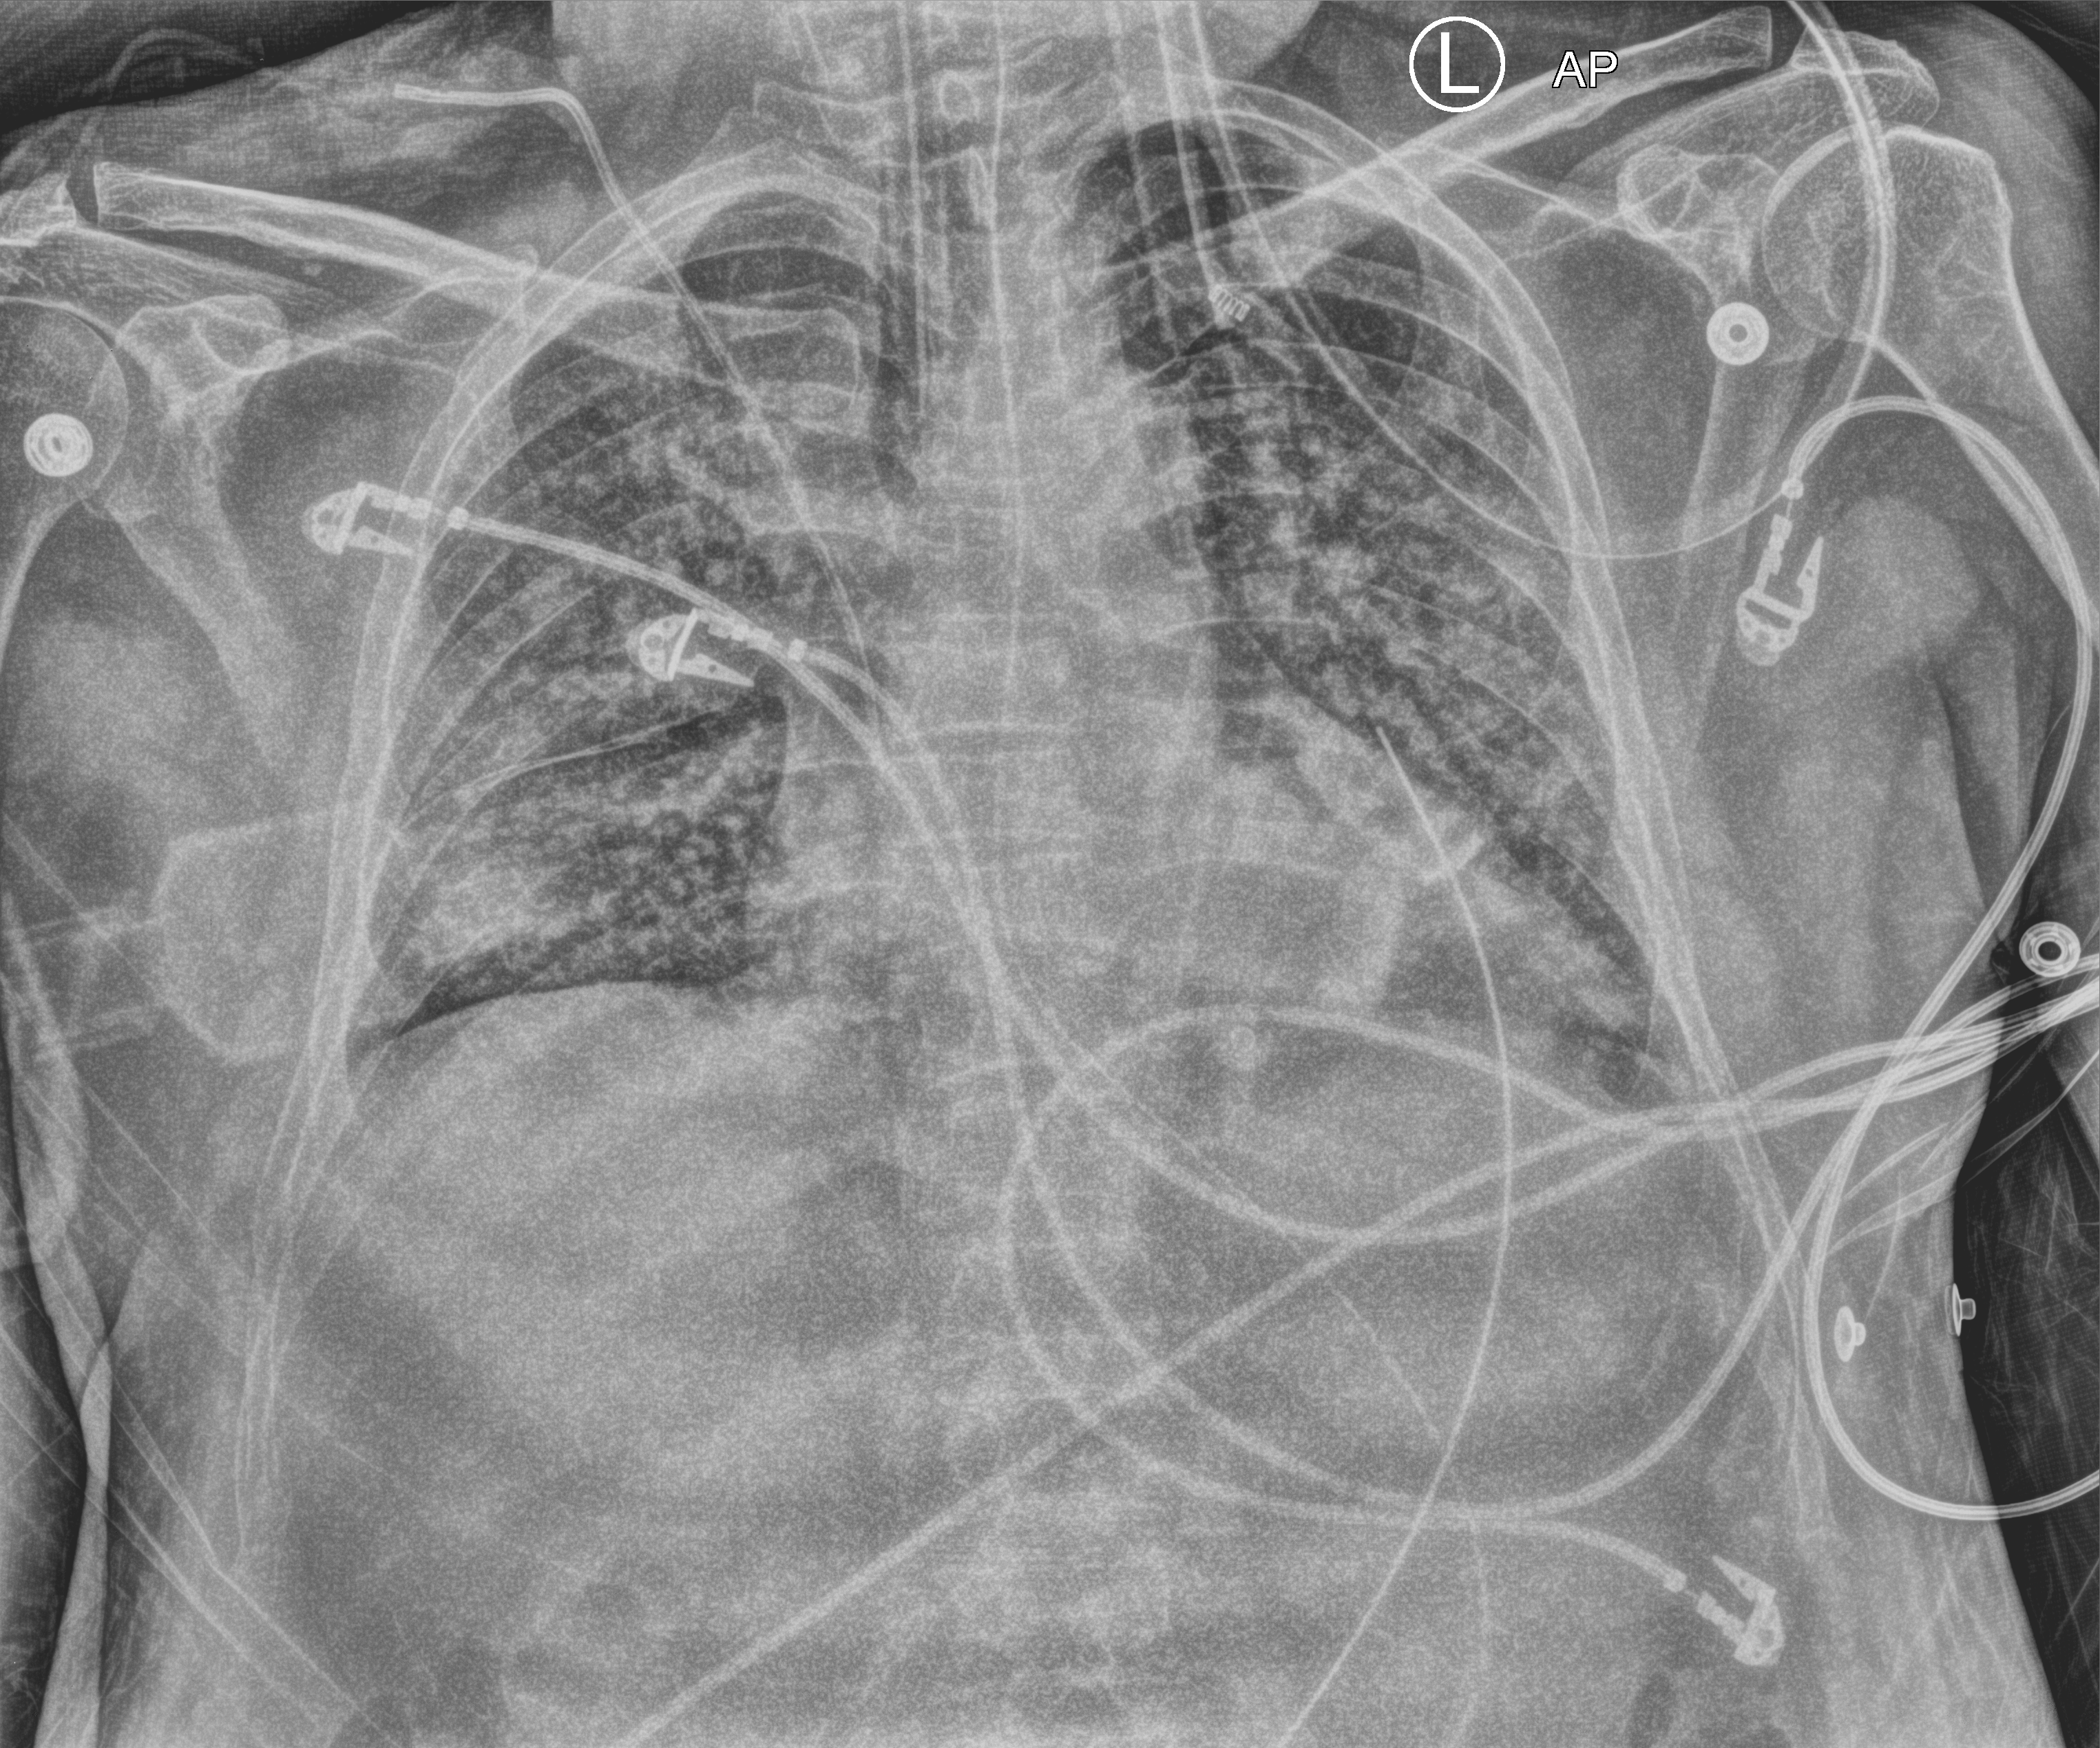
Portable chest radiograph, anteroposterior (AP) projection. Patient hospitalised with COVID-19; male, aged 60–74 years.
Admission-level facts for this patient (not findings on this image; timing relative to this image not recorded): admitted to intensive care during this hospital stay: yes.